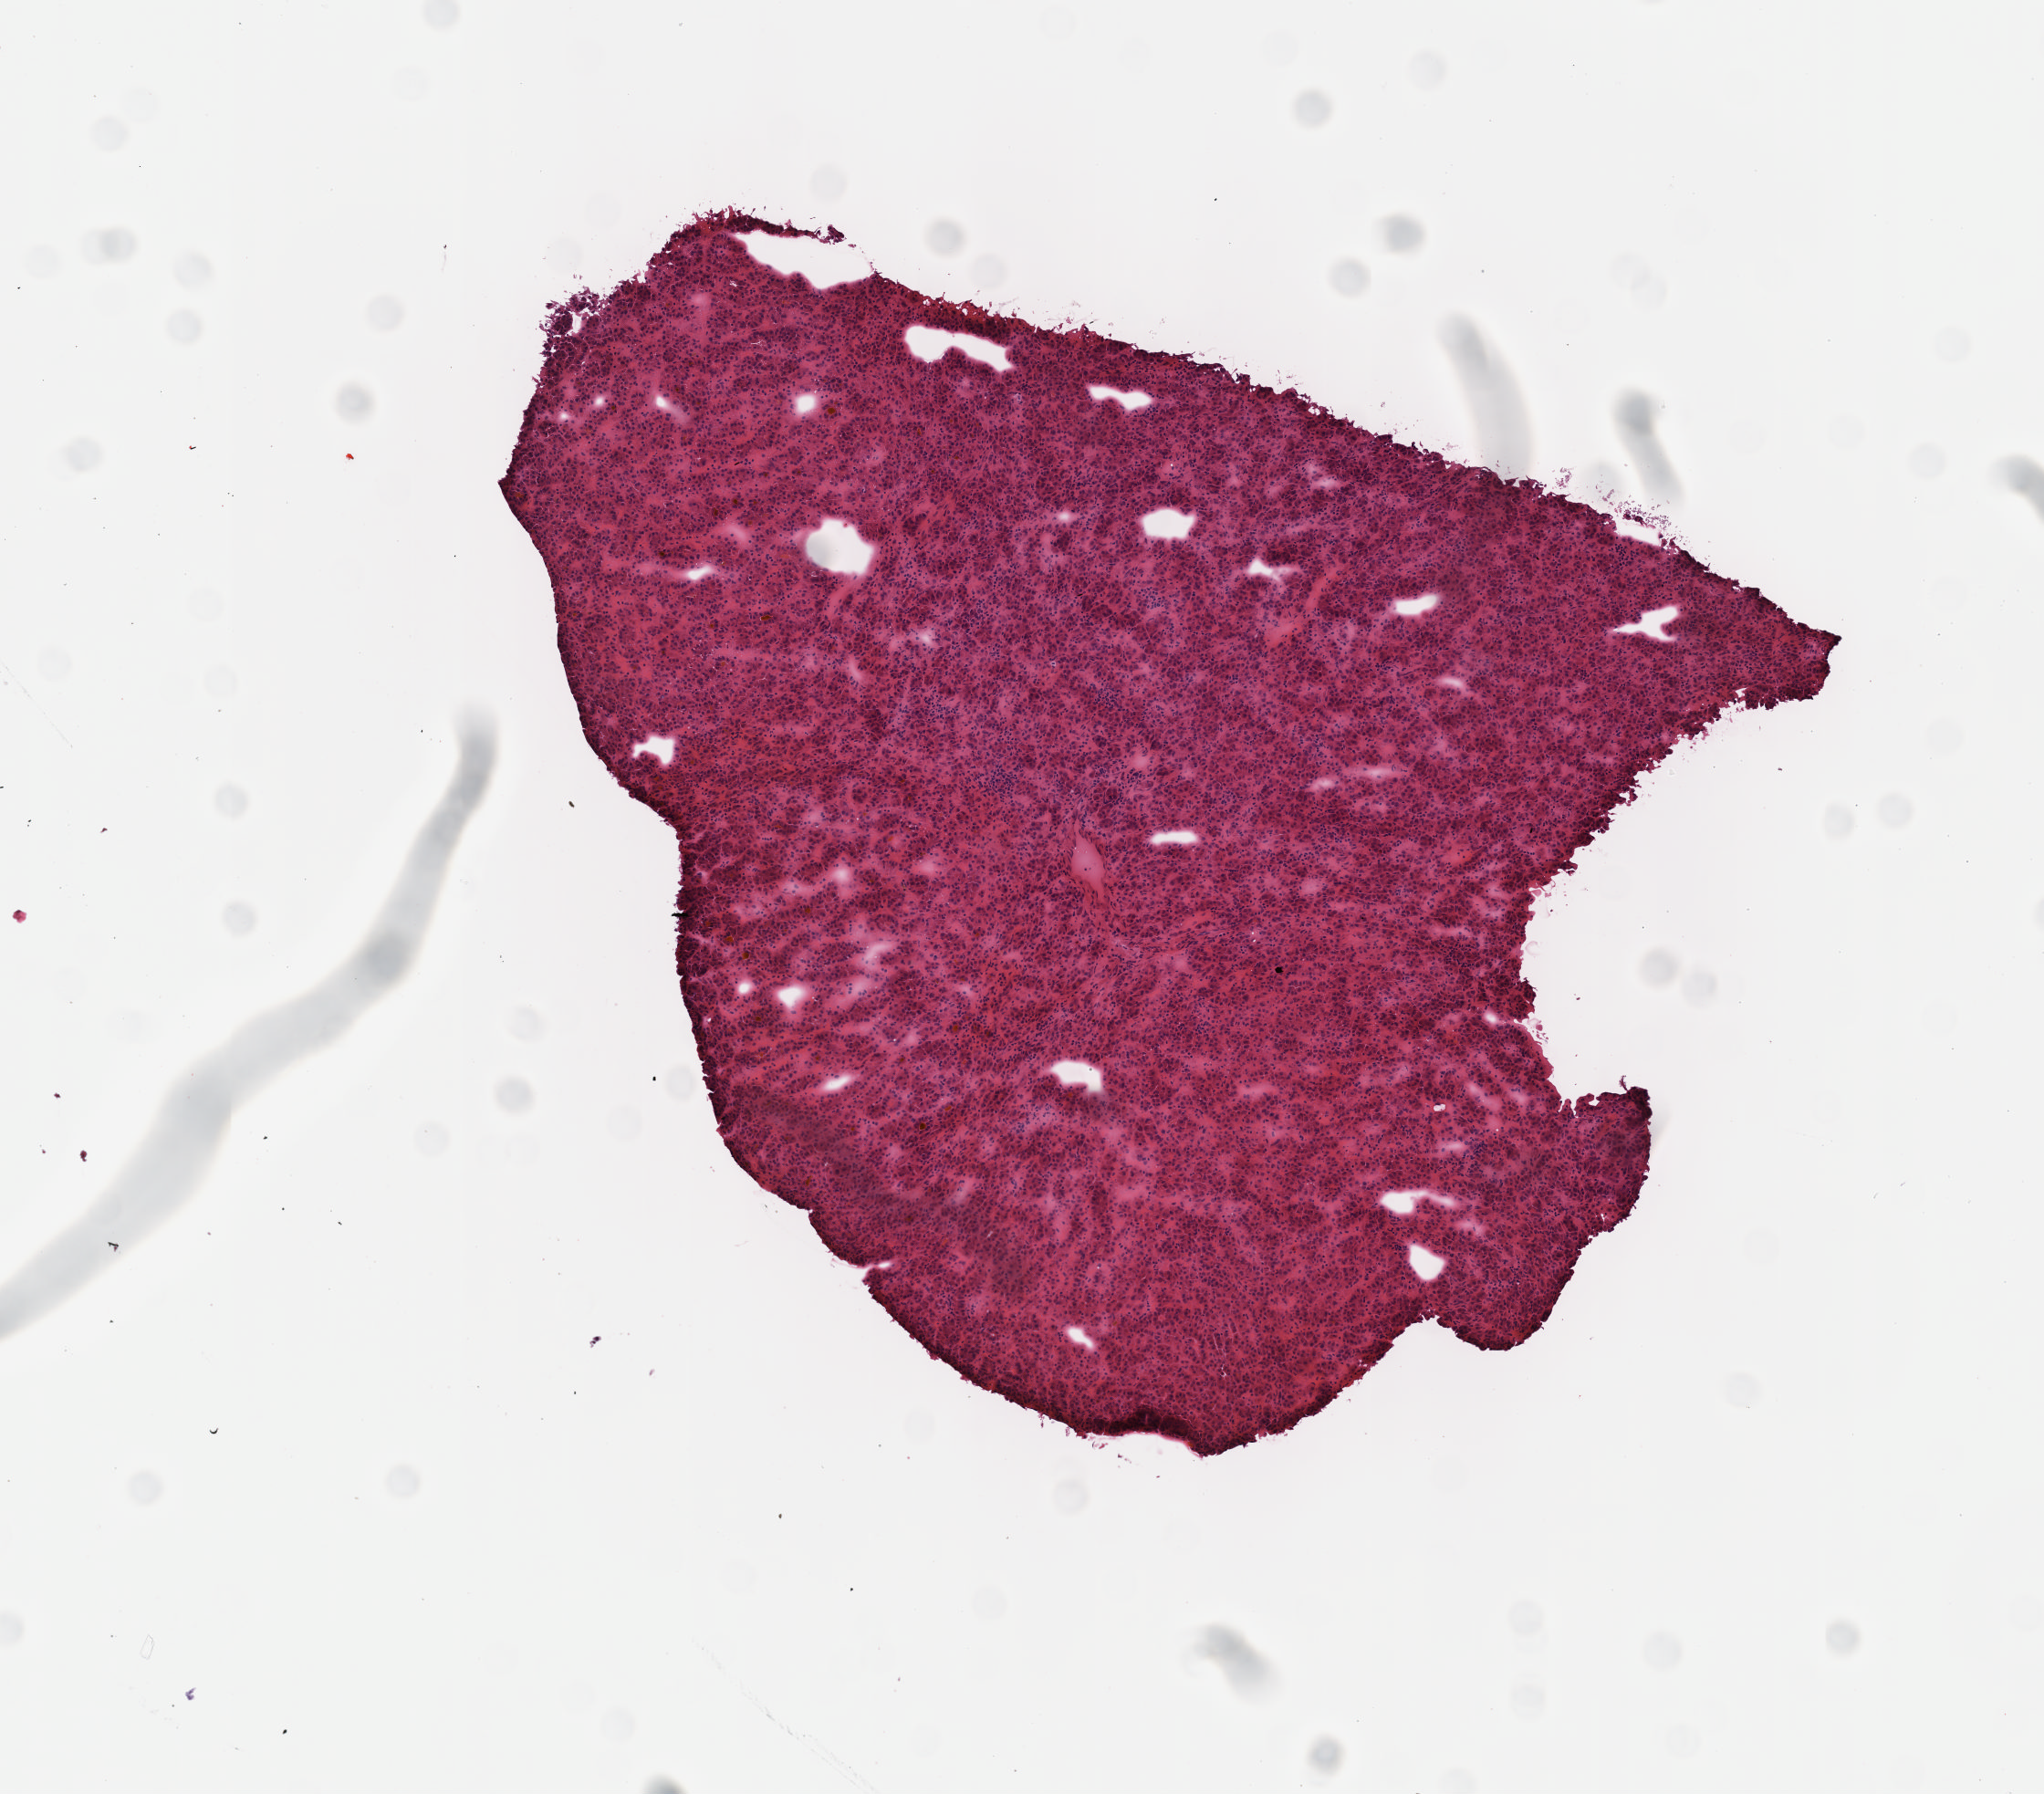
Digitized H&E-stained tissue section (whole slide) — a low-resolution overview of the entire scanned area, about 4.5 x 4.0 mm (from a 40x scan), frozen section from the top of the tissue portion, sample: primary tumour, liver. Male patient; age at initial diagnosis 73 years.
Pathologic diagnosis: Hepatocellular carcinoma, NOS.